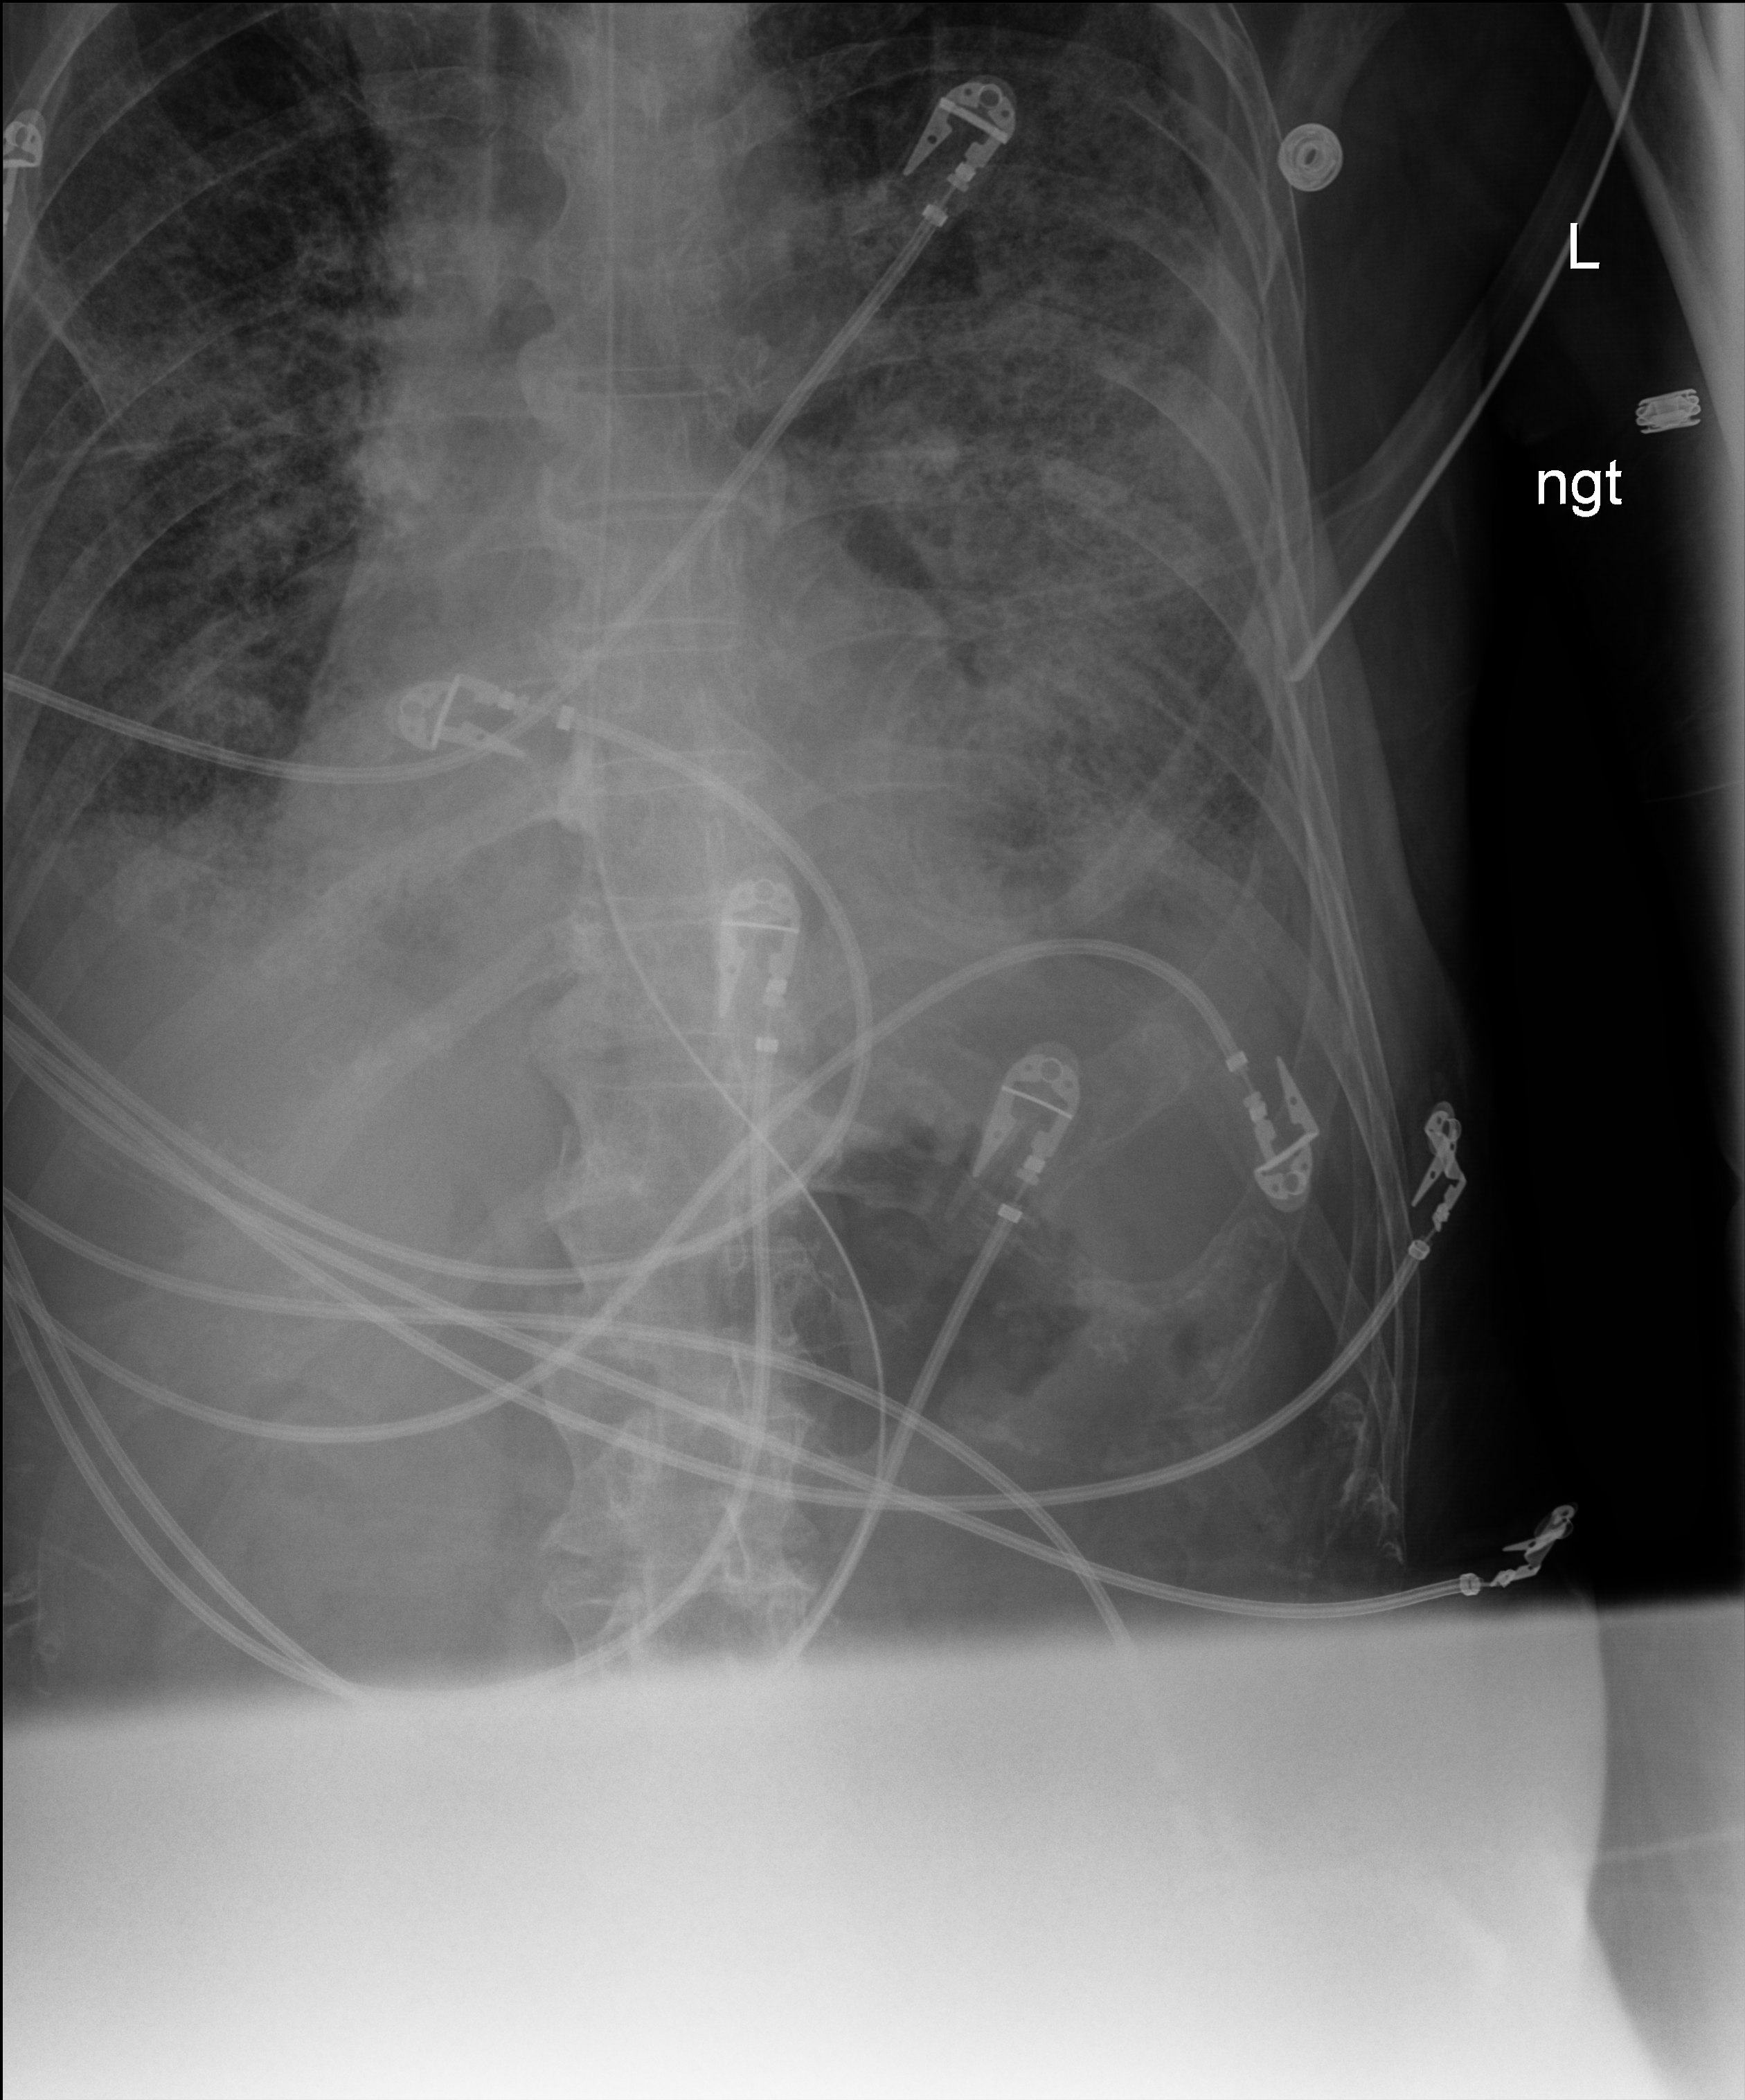
Portable chest radiograph; anteroposterior (AP) projection. Patient hospitalised with COVID-19; male, aged 60–74 years.
Admission-level facts for this patient (not findings on this image; timing relative to this image not recorded):
- mechanically ventilated during this hospital stay: yes
- admitted to intensive care during this hospital stay: yes